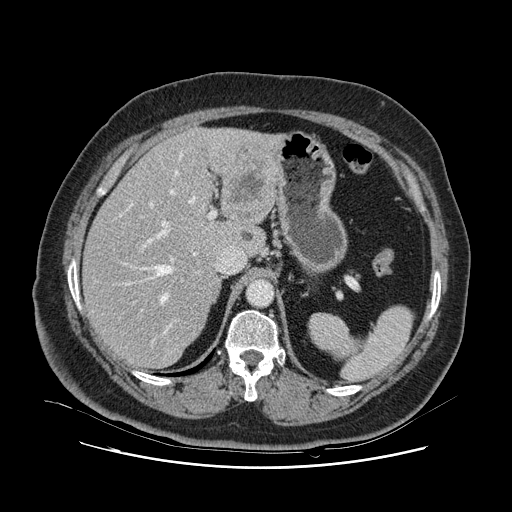
Contrast-enhanced abdominal CT, one axial slice; slice 76 of 132 in the series (ordered by position); 120 kVp; soft-tissue window (W 400 / L 40 HU); 512 × 512 image matrix, field of view 391 × 391 mm. Female patient, age 73 years. From the clinical record (not read from this slice): diagnosis: colorectal cancer liver metastases, imaged before liver resection; multiple liver metastases: no; largest metastasis: 7 cm; chemotherapy before resection: yes.
Outlined on this slice (manually delineated by an expert):
- hepatic veins: bounding box [x1, y1, x2, y2] px = [126, 153, 196, 343]
- liver: [84, 128, 275, 368]
- planned liver remnant (the part of the liver to remain after resection): [84, 158, 239, 368]
- portal vein (with intrahepatic branches): [142, 202, 216, 334]
- liver metastasis: [242, 233, 253, 242]
- liver metastasis: [227, 159, 266, 218]